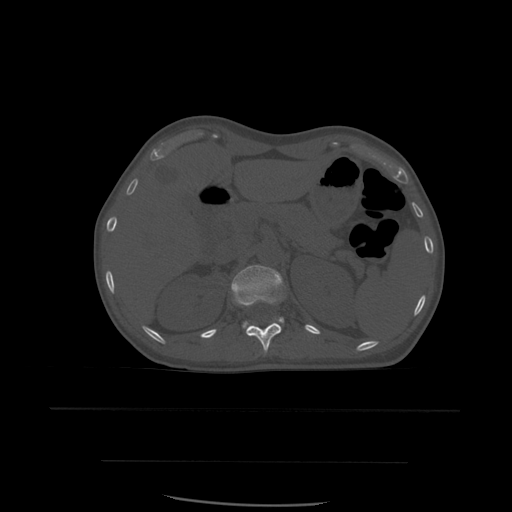
CT including the spine, one axial slice. Slice 264 of 574 in the series (ordered by position). Bone window (W 1800 / L 400 HU). 1.25 mm slice thickness. 512 × 512 image matrix, field of view 392 × 392 mm. Patient age 48 years. Case-level facts recorded for this patient, not image findings: primary cancer: lung; vertebrae with lytic lesions (as recorded): T11.
Annotated regions visible in this slice (semi-automatic segmentation, software-assisted and operator-edited):
- L1 vertebra: bounding box [x1, y1, x2, y2] px = [231, 265, 284, 332]
- T12 vertebra: [246, 323, 282, 355]